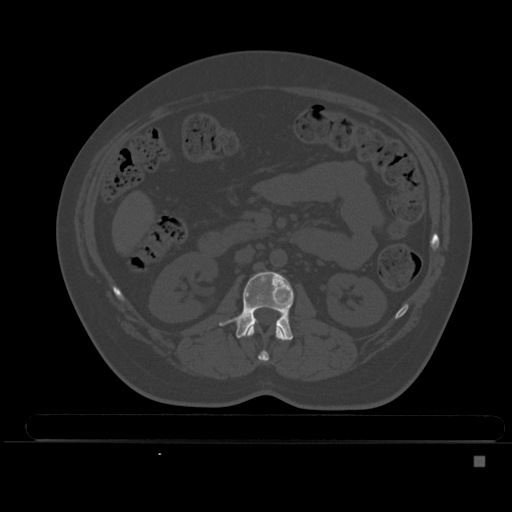
CT including the spine, one axial slice; slice 180 of 495 in the series (ordered by position); bone window (W 1800 / L 400 HU); 512 × 512 image matrix, field of view 404 × 404 mm. Patient: female, 33 years. Case-level facts recorded for this patient, not image findings: primary cancer: breast.
Outlined on this slice (semi-automatically segmented with operator editing):
- L1 vertebra: bounding box [x1, y1, x2, y2] px = [245, 326, 285, 362]
- L2 vertebra: [219, 271, 294, 341]